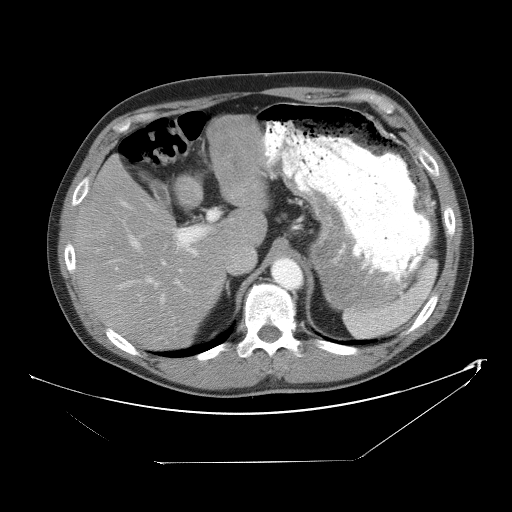
Contrast-enhanced abdominal CT, one axial slice; slice 36 of 53 in the series (ordered by position); reconstruction kernel STANDARD; 120 kVp; intravenous contrast given; soft-tissue window (W 400 / L 40 HU); 5 mm slice thickness; 512 × 512 image matrix, field of view 438 × 438 mm. Male patient, age 59 years. Case-level facts recorded for this patient, not image findings: diagnosis: colorectal cancer liver metastases, imaged before liver resection; multiple liver metastases: yes; largest metastasis: 8.5 cm; disease in both lobes: no.
Outlined on this slice (manually delineated by an expert):
- hepatic veins: box from (x=119, y=230) to (x=183, y=289) px
- liver: (x=75, y=117)–(x=265, y=350)
- planned liver remnant (the part of the liver to remain after resection): (x=76, y=158)–(x=233, y=350)
- portal vein (with intrahepatic branches): (x=116, y=200)–(x=217, y=292)